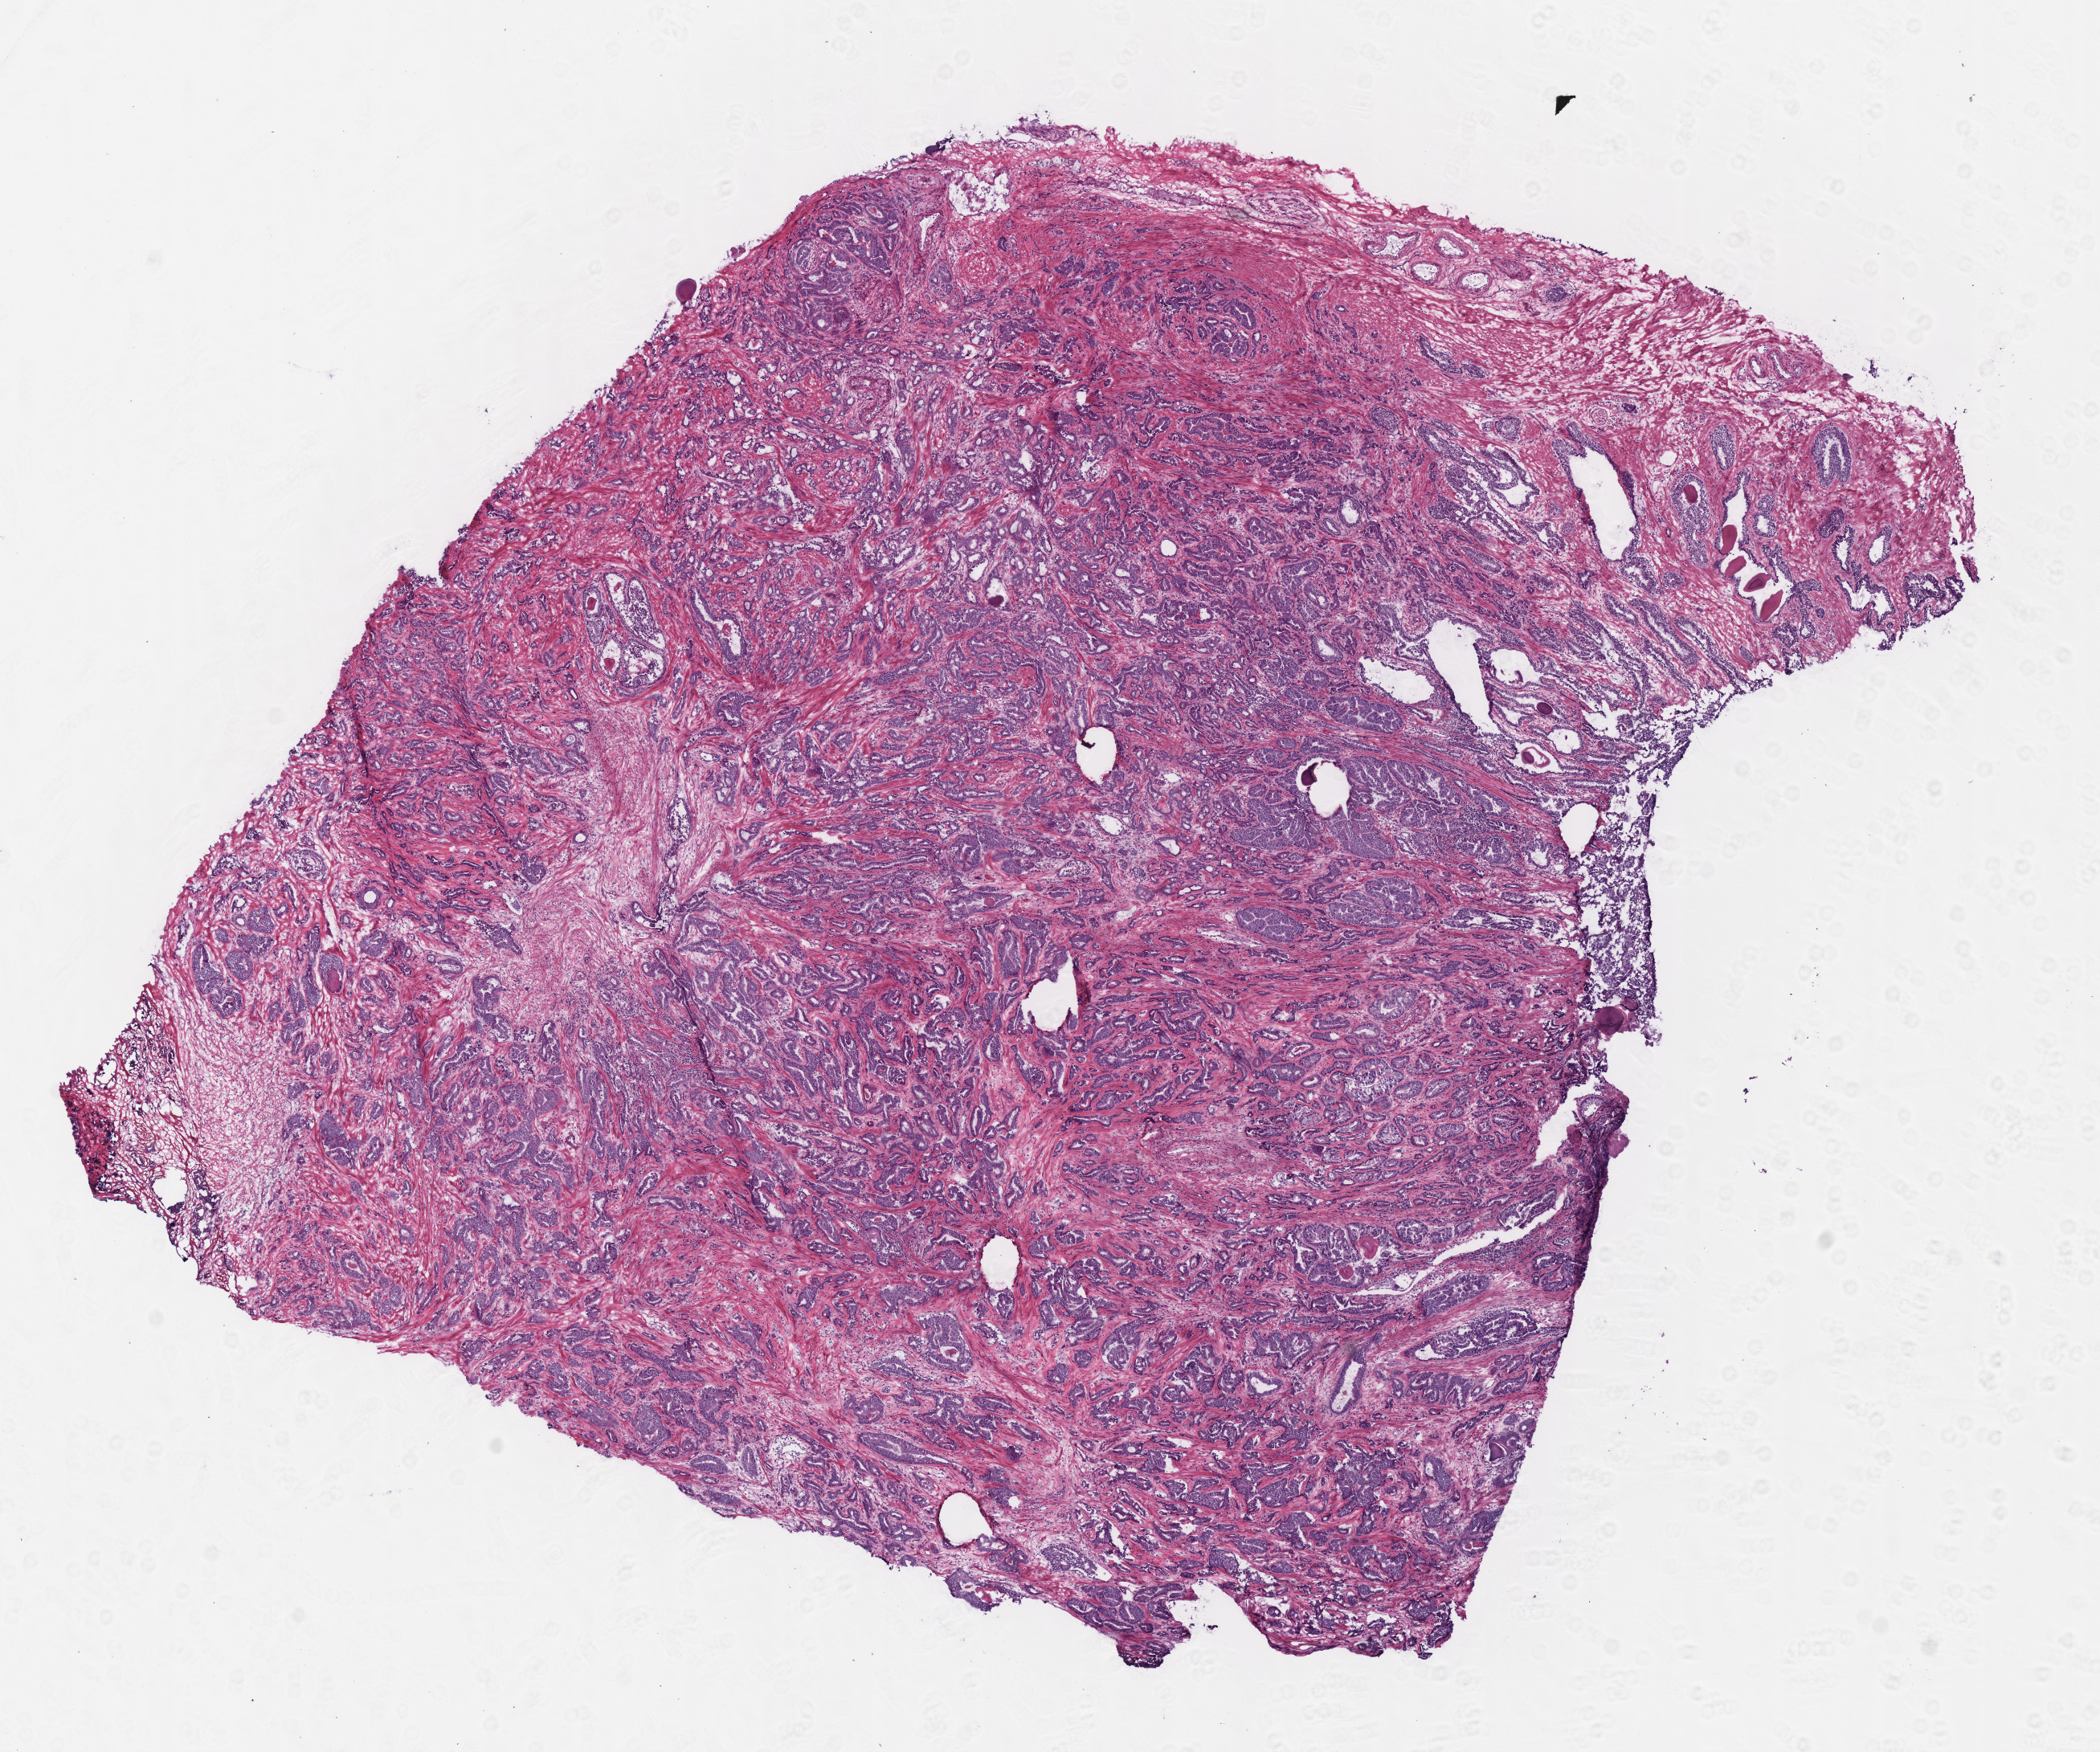
Whole-slide histology image, Hematoxylin and eosin (H&E) stained, whole scanned area (about 10.3 x 8.6 mm, from a 40x scan) shown as a low-resolution overview, frozen section, primary tumour sample from the prostate. Male patient; age at initial diagnosis 60 years. Gleason score: 6 (3+3).
- laterality: right
- pathologic diagnosis: Acinar cell carcinoma